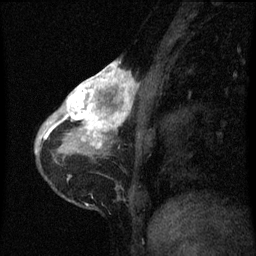
Breast MRI (dynamic contrast-enhanced), one sagittal slice. Slice 18 of 60 in the series (ordered by position). Dynamic contrast-enhanced series, image 2 of 3 at this slice position (ordered by acquisition). 1.5 T. TE 4.2 ms, TR 8 ms. 256 × 256 image matrix, field of view 180 × 180 mm. Female patient, age 38 years.
Outlined on this slice (semi-automatic segmentation, software-assisted and operator-edited):
- analysis volume of interest (the breast-tissue region the enhancement analysis was run in; not a lesion): bounding box <61,64,137,147> (left, top, right, bottom; pixels)
- tumour enhancement mask (voxels above the 70 % enhancement threshold inside the analysis volume of interest): <61,64,137,147>